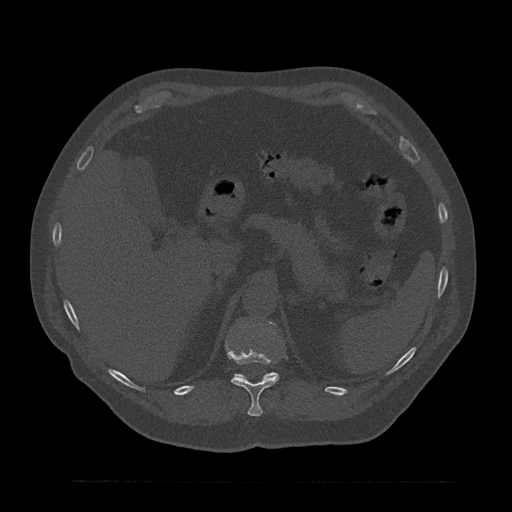
CT including the spine, one axial slice; slice 273 of 797 in the series (ordered by position); bone window (W 1800 / L 400 HU); 0.5 mm slice thickness; 512 × 512 image matrix. Male patient, age 61 years. From the clinical record (not read from this slice): primary cancer: prostate.
Structures marked on this image (semi-automatic segmentation, software-assisted and operator-edited):
- T11 vertebra: bounding box <226,342,279,417> (left, top, right, bottom; pixels)
- T12 vertebra: <236,372,277,378>